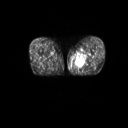
FDG PET of an extremity soft-tissue mass (from a PET/CT study), one axial slice. Position 14 of 267 along the scan axis. 3.27 mm slice thickness. 128 × 128 image matrix, field of view 600 × 600 mm. Male patient, age 59 years. Case-level facts recorded for this patient, not image findings: histological type: pleiomorphic liposarcoma; grade: high; site of the primary tumour: left thigh.
Outlined on this slice (expert contour drawn on MRI and transferred to this co-registered scan by the dataset authors):
- gross tumour volume including surrounding oedema: bounding box <74,53,89,69> (left, top, right, bottom; pixels)
- gross tumour volume (mass): <77,62,85,67>